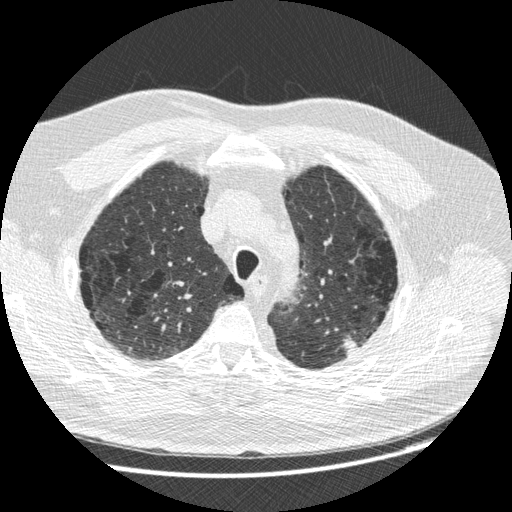
Low-dose screening chest CT, one axial slice. Position 207 of 258 along the scan axis. Lung window (W 1500 / L -600 HU). 512 × 512 image matrix.
Outlined on this slice (outlined manually by an expert reader):
- lesion 1 (tumor, upper lobe of left lung): bounding box (x1, y1, x2, y2) in pixels: (342, 336, 357, 356)